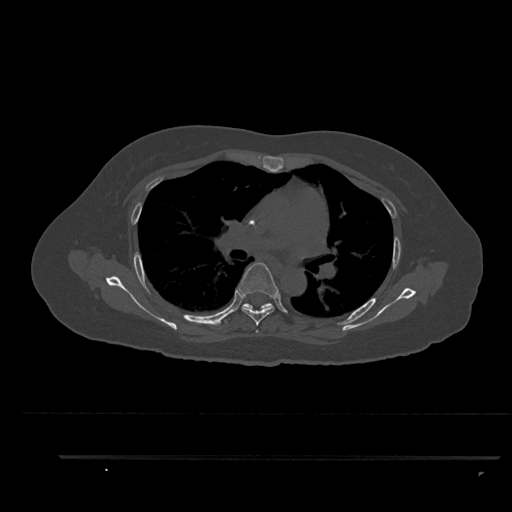
CT including the spine, one axial slice; position 589 of 797 along the scan axis; reconstruction kernel Br40s/3; 120 kVp; bone window (W 1800 / L 400 HU); 0.5 mm slice thickness; 512 × 512 image matrix. Patient: female, 44 years. Case-level facts recorded for this patient, not image findings: primary cancer: renal.
Annotated regions visible in this slice (semi-automatically segmented with operator editing):
- T4 vertebra: bounding box (x1, y1, x2, y2) in pixels: (256, 330, 258, 333)
- T5 vertebra: (238, 262, 278, 326)
- T6 vertebra: (242, 303, 273, 311)